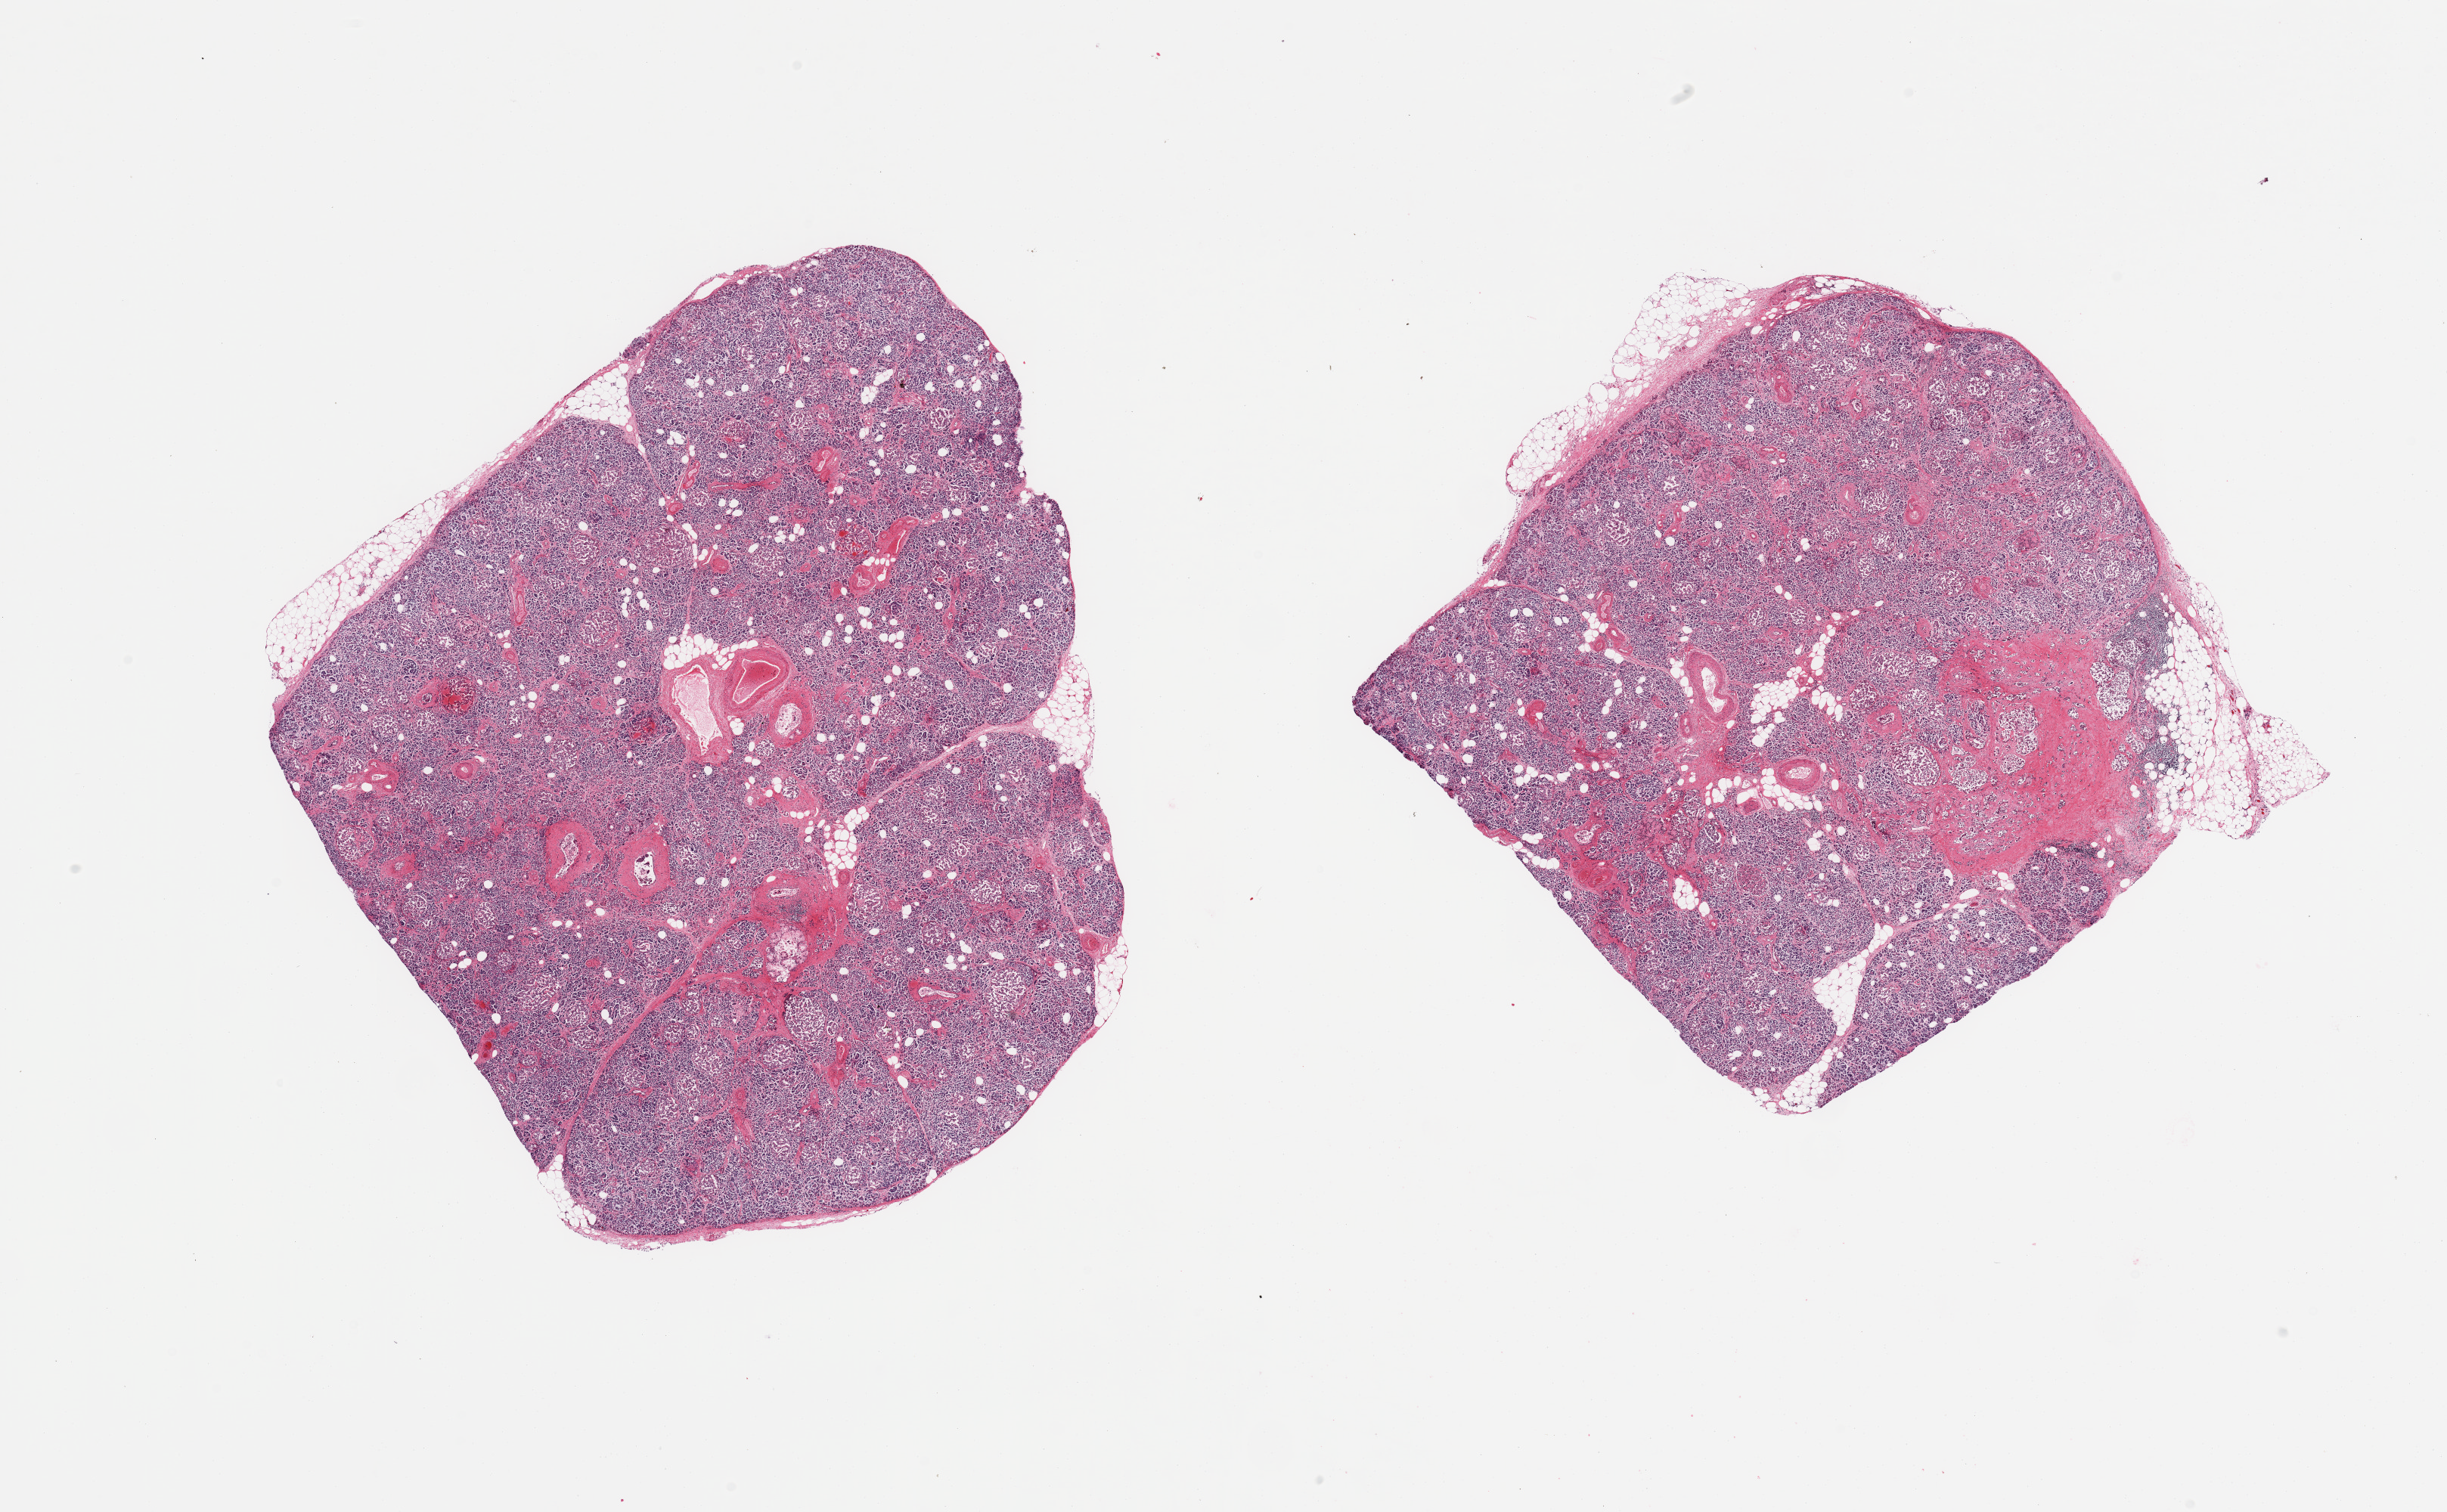
Hematoxylin and eosin (H&E) whole-slide image, whole scanned area (about 25.6 x 15.8 mm, from a 20x scan) shown as a low-resolution overview; PAXgene-fixed paraffin-embedded (PFPE) section; target tissue: pancreas; tissue donor sample. Donor: male.
Pathologist's review note for this sample: 2 pieces; endocrine elements better preserved than exocrine.